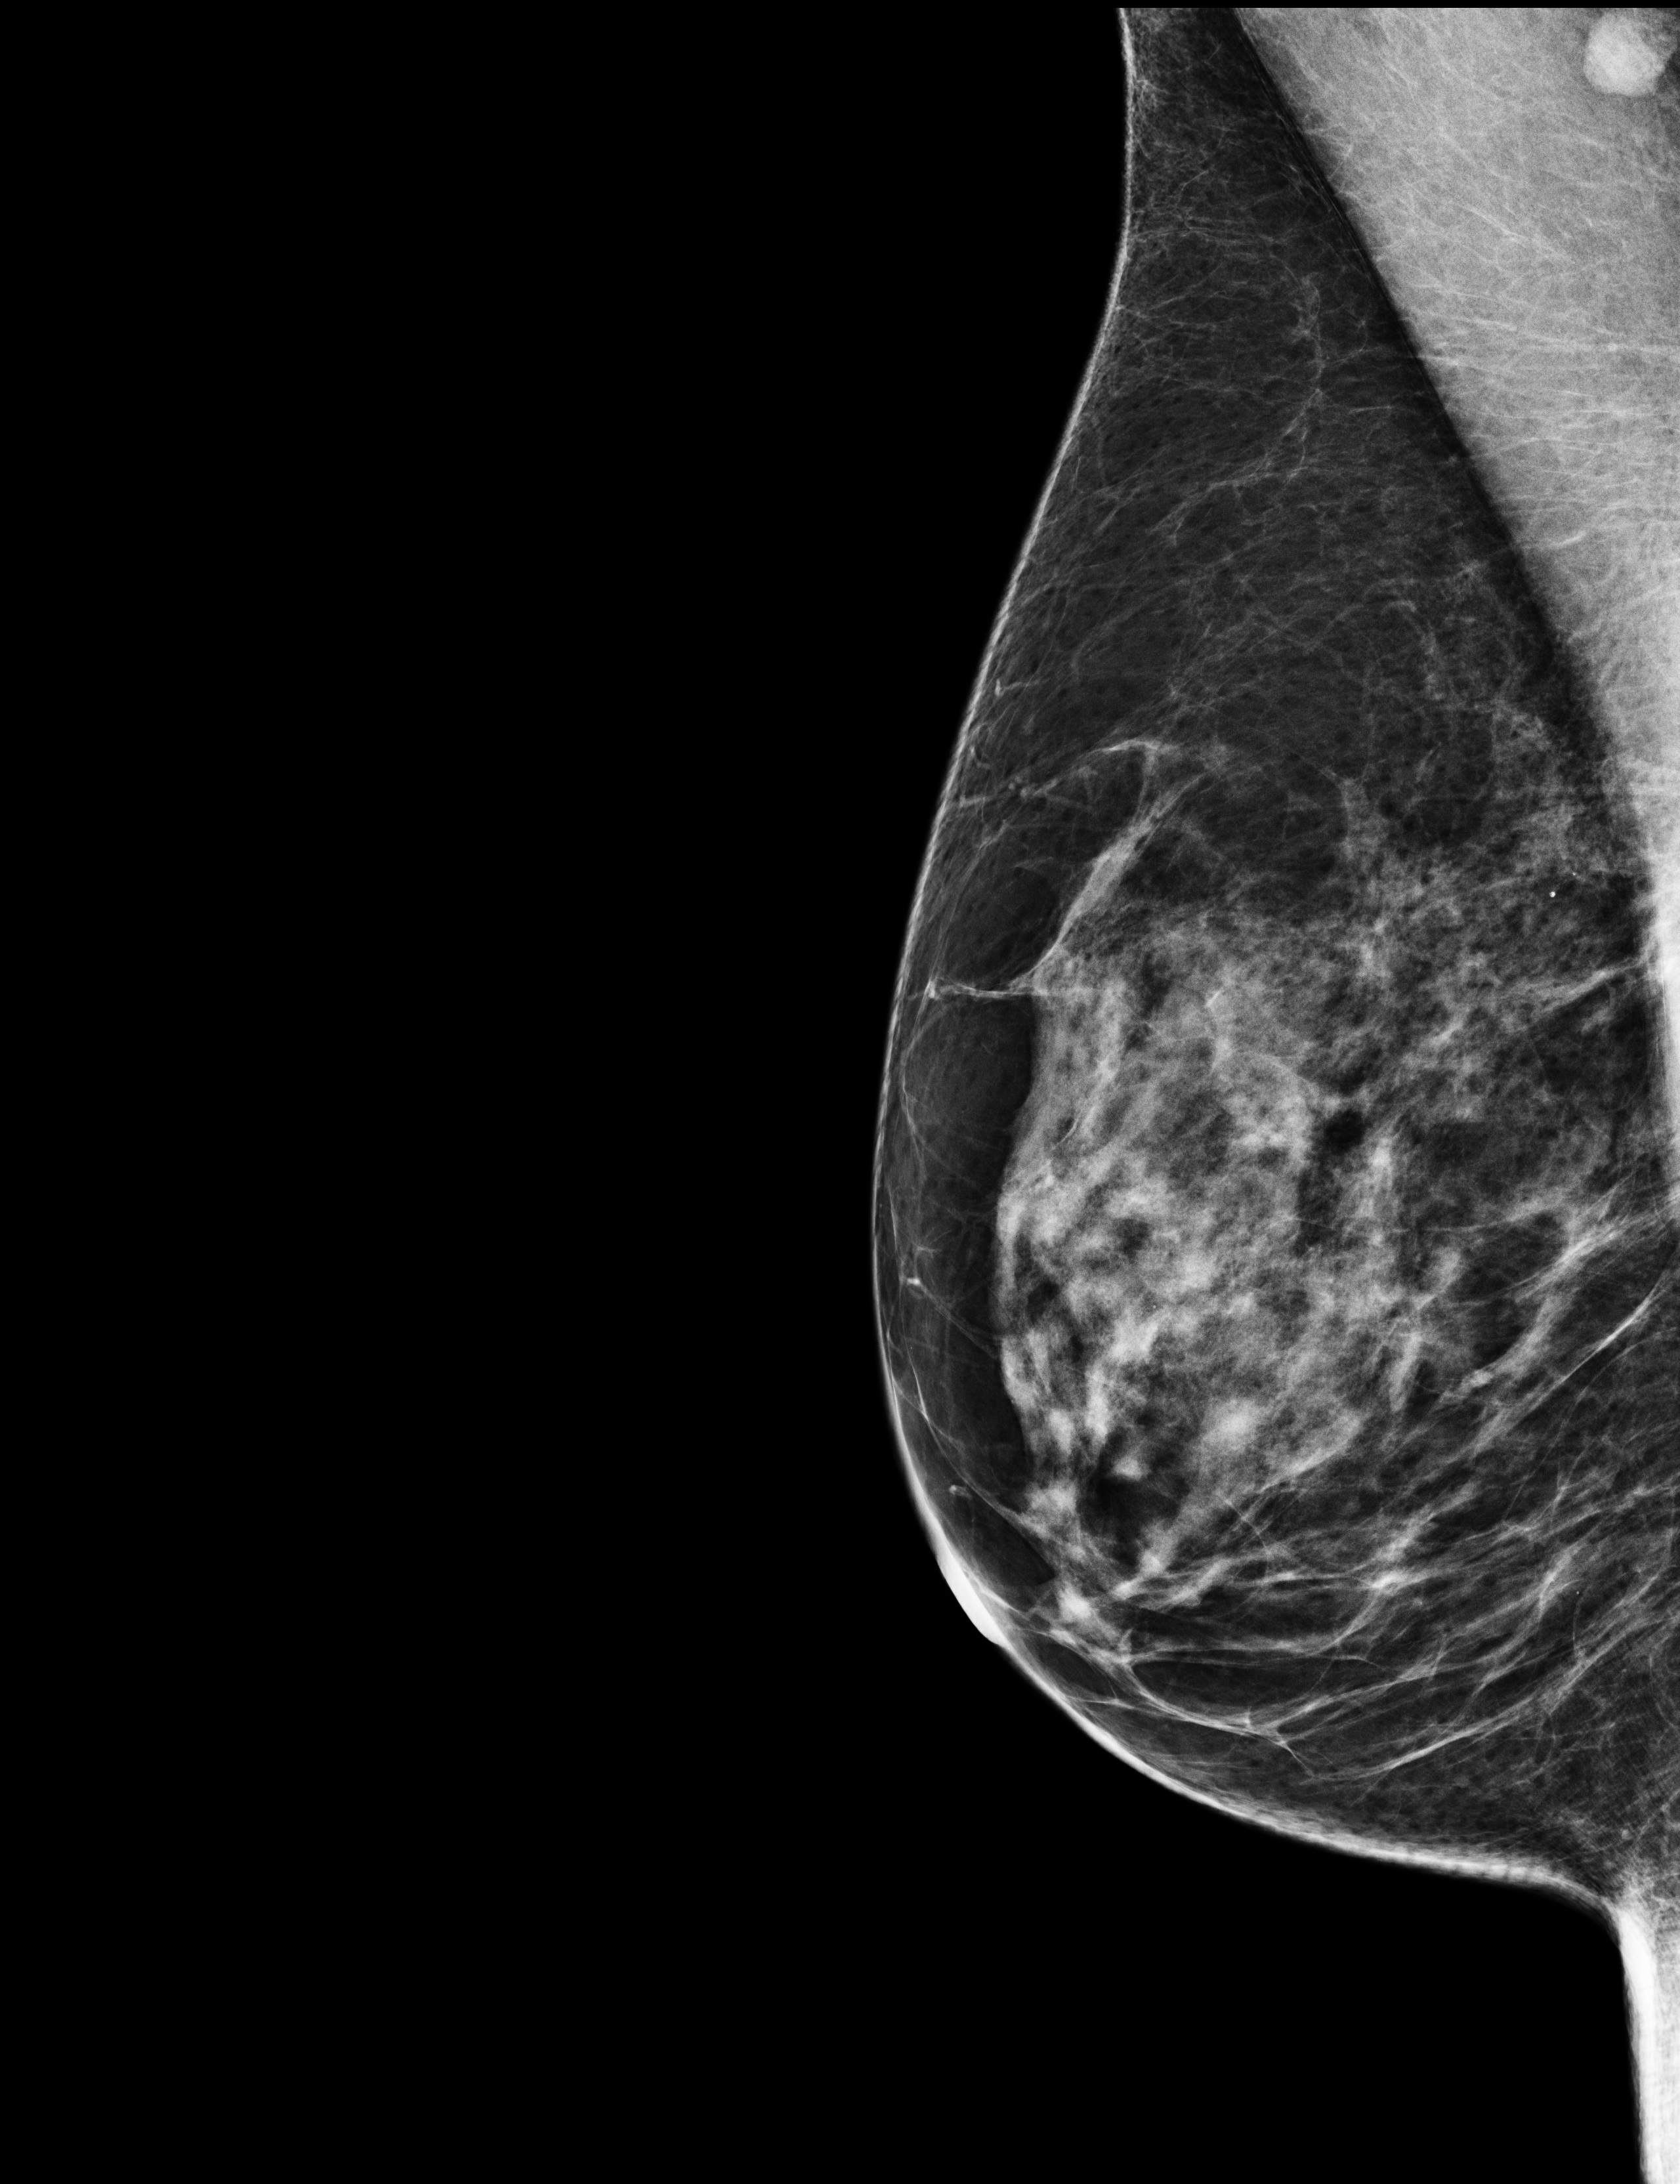
Screening examination.
Image type: full-field digital mammogram. Breast: right. Projection: medio-lateral oblique projection.